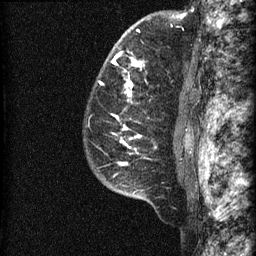
Breast MRI (dynamic contrast-enhanced), one sagittal slice; slice 50 of 60 in the series (ordered by position); dynamic contrast-enhanced series, image 2 of 3 at this slice position (ordered by acquisition); 1.5 T; TE 4.2 ms, TR 22.7 ms; 1.5 mm slice thickness; 256 × 256 image matrix, field of view 180 × 180 mm. Patient: female, 48 years. From the clinical record (not read from this slice): setting: breast cancer imaged before/during neoadjuvant chemotherapy; receptor status: triple-negative.
Annotated regions visible in this slice (semi-automatically segmented with operator editing):
- analysis volume of interest (the breast-tissue region the enhancement analysis was run in; not a lesion): bounding box (x1, y1, x2, y2) in pixels: (83, 23, 186, 202)
- tumour enhancement mask (voxels above the 90 % enhancement threshold inside the analysis volume of interest): (99, 29, 141, 176)